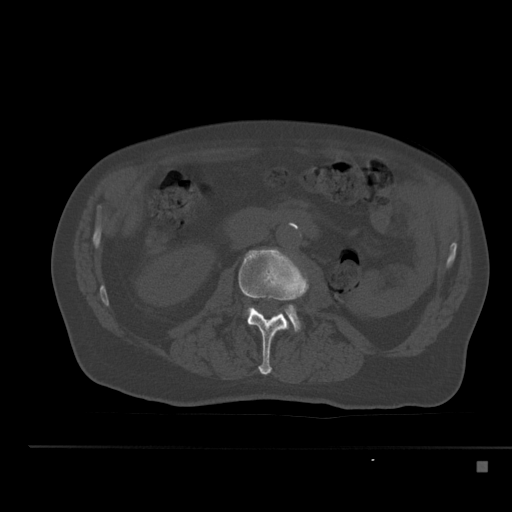
CT including the spine, one axial slice. 120 kVp. Bone window (W 1800 / L 400 HU). 512 × 512 image matrix, field of view 408 × 408 mm. Patient: male, 70 years. From the clinical record (not read from this slice): primary cancer: renal; vertebrae with lytic lesions (as recorded): T4, T6, T10, T12, L3, L4, L5.
Outlined on this slice (semi-automatic segmentation, software-assisted and operator-edited):
- L2 vertebra: bounding box <239,248,309,375> (left, top, right, bottom; pixels)
- L3 vertebra: <286,305,300,331>